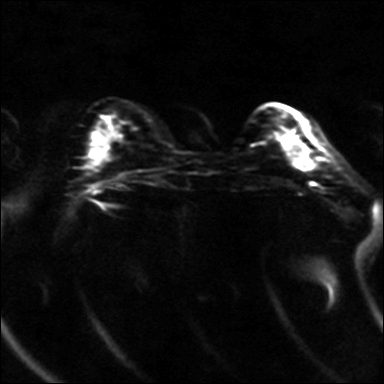
Breast MRI, one axial slice; position 10 of 36 along the scan axis; diffusion-weighted series; image 2 of 4 stored at this slice position (different b-values; order by instance number); 3 T; 4 mm slice thickness; 384 × 384 image matrix, field of view 320 × 320 mm. Female patient.
Structures marked on this image (outlined manually by an expert reader):
- tumour on diffusion-weighted imaging: bounding box <289,140,300,160> (left, top, right, bottom; pixels)